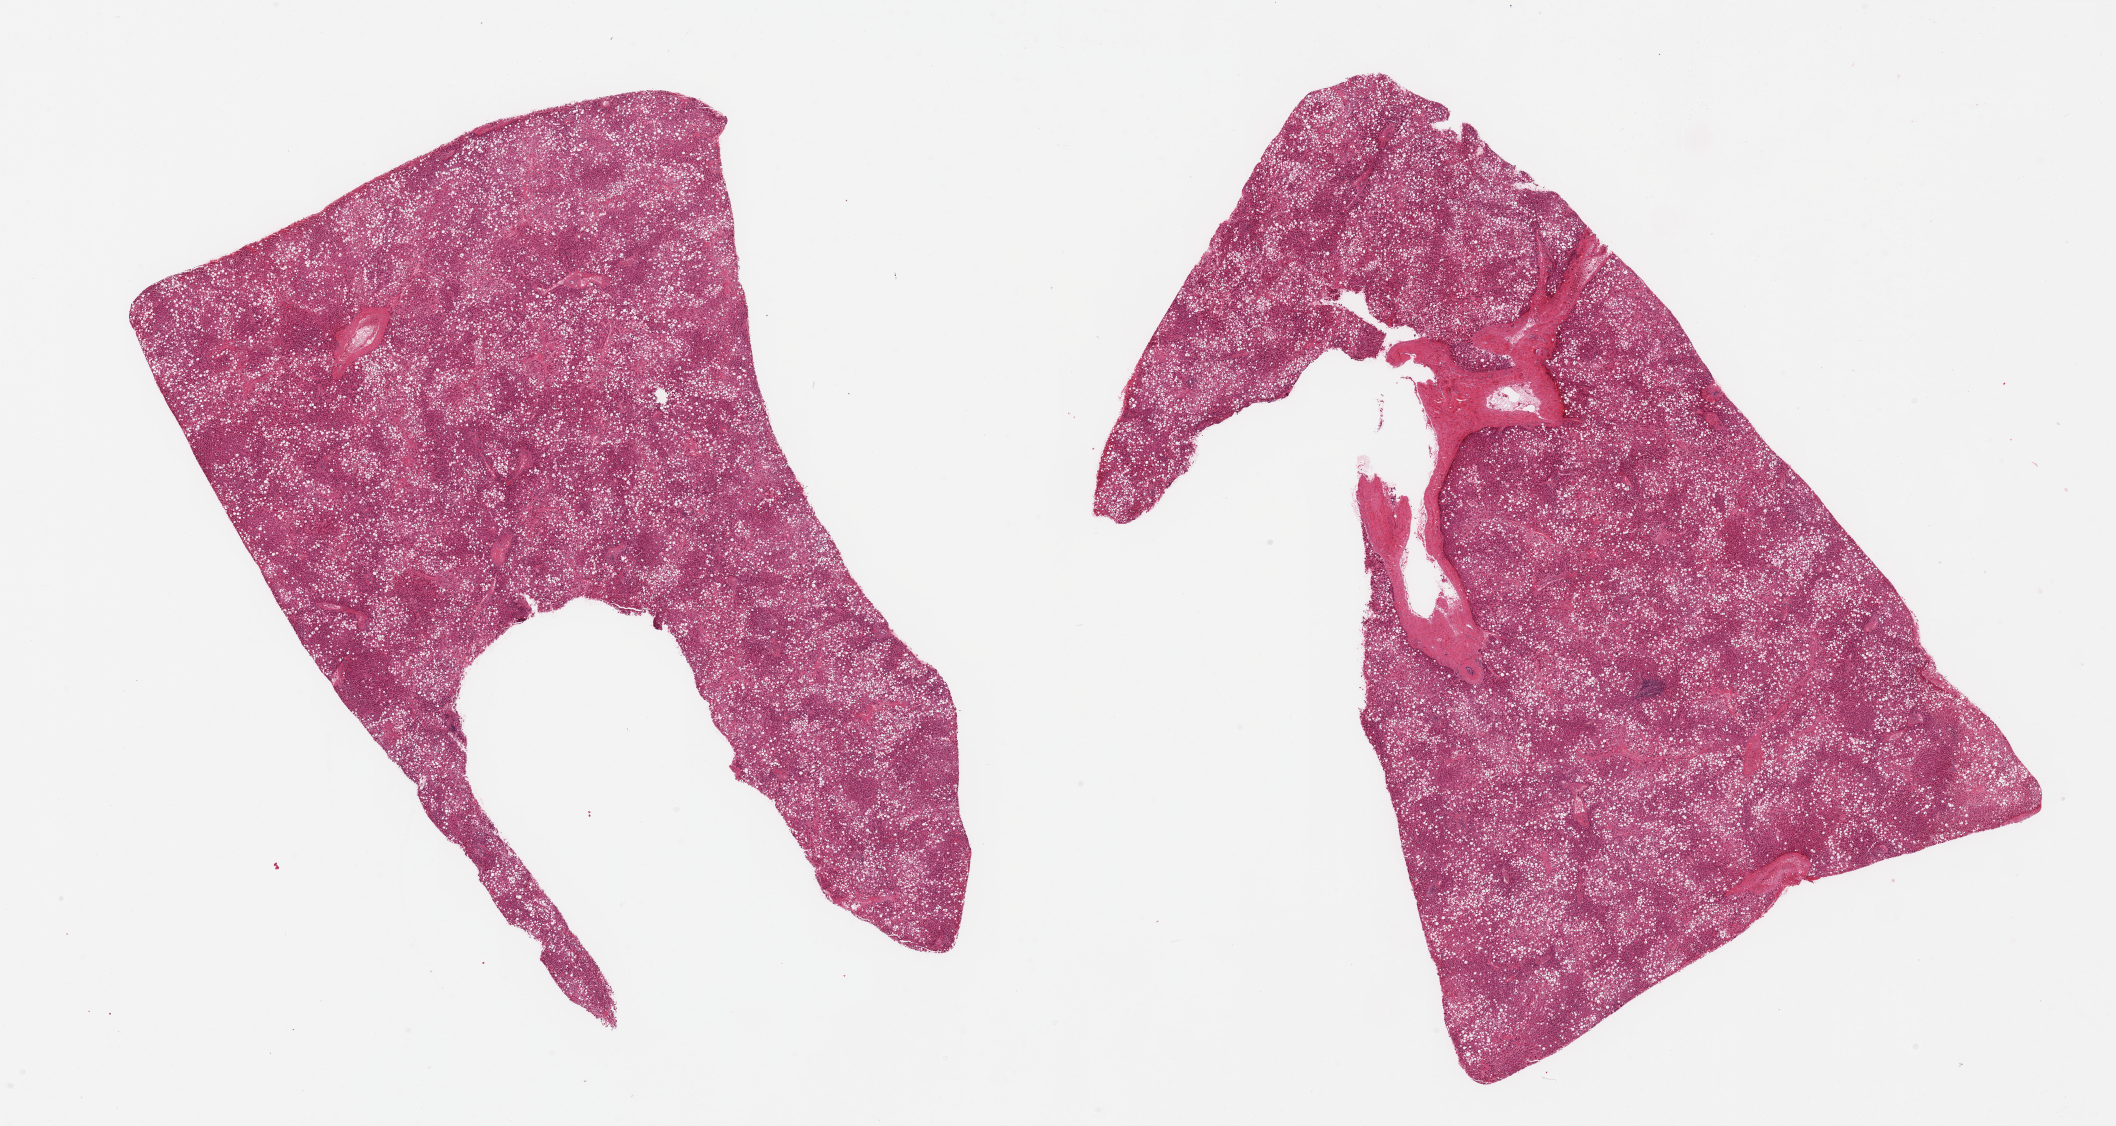
Haematoxylin and eosin whole-slide image — shown as a low-resolution overview of the whole scanned area (about 33.5 x 17.8 mm, from a 20x scan). PAXgene-fixed paraffin-embedded (PFPE) section. Target tissue: liver. Donor tissue sample. Male donor.
- review note (as recorded): 2 pieces, approaching score '2': diffuse severe macrovesicular steatosis